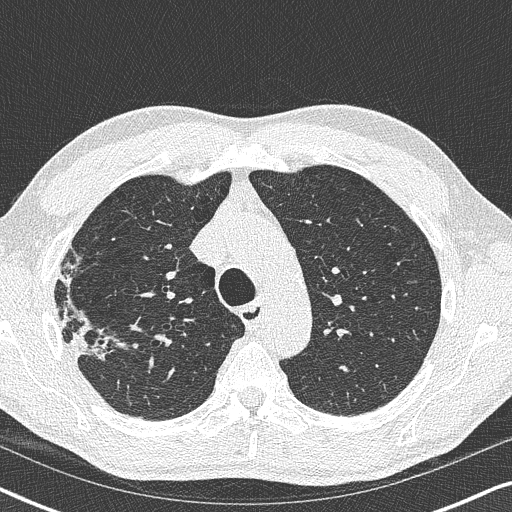
Low-dose screening chest CT, one axial slice; position 271 of 356 along the scan axis; reconstruction kernel B50f; lung window (W 1500 / L -600 HU); 1 mm slice thickness; 512 × 512 image matrix, field of view 330 × 330 mm.
Structures marked on this image (manually delineated by an expert):
- lesion 1 (tumor, upper lobe of right lung): bounding box (x1, y1, x2, y2) in pixels: (58, 299, 119, 361)